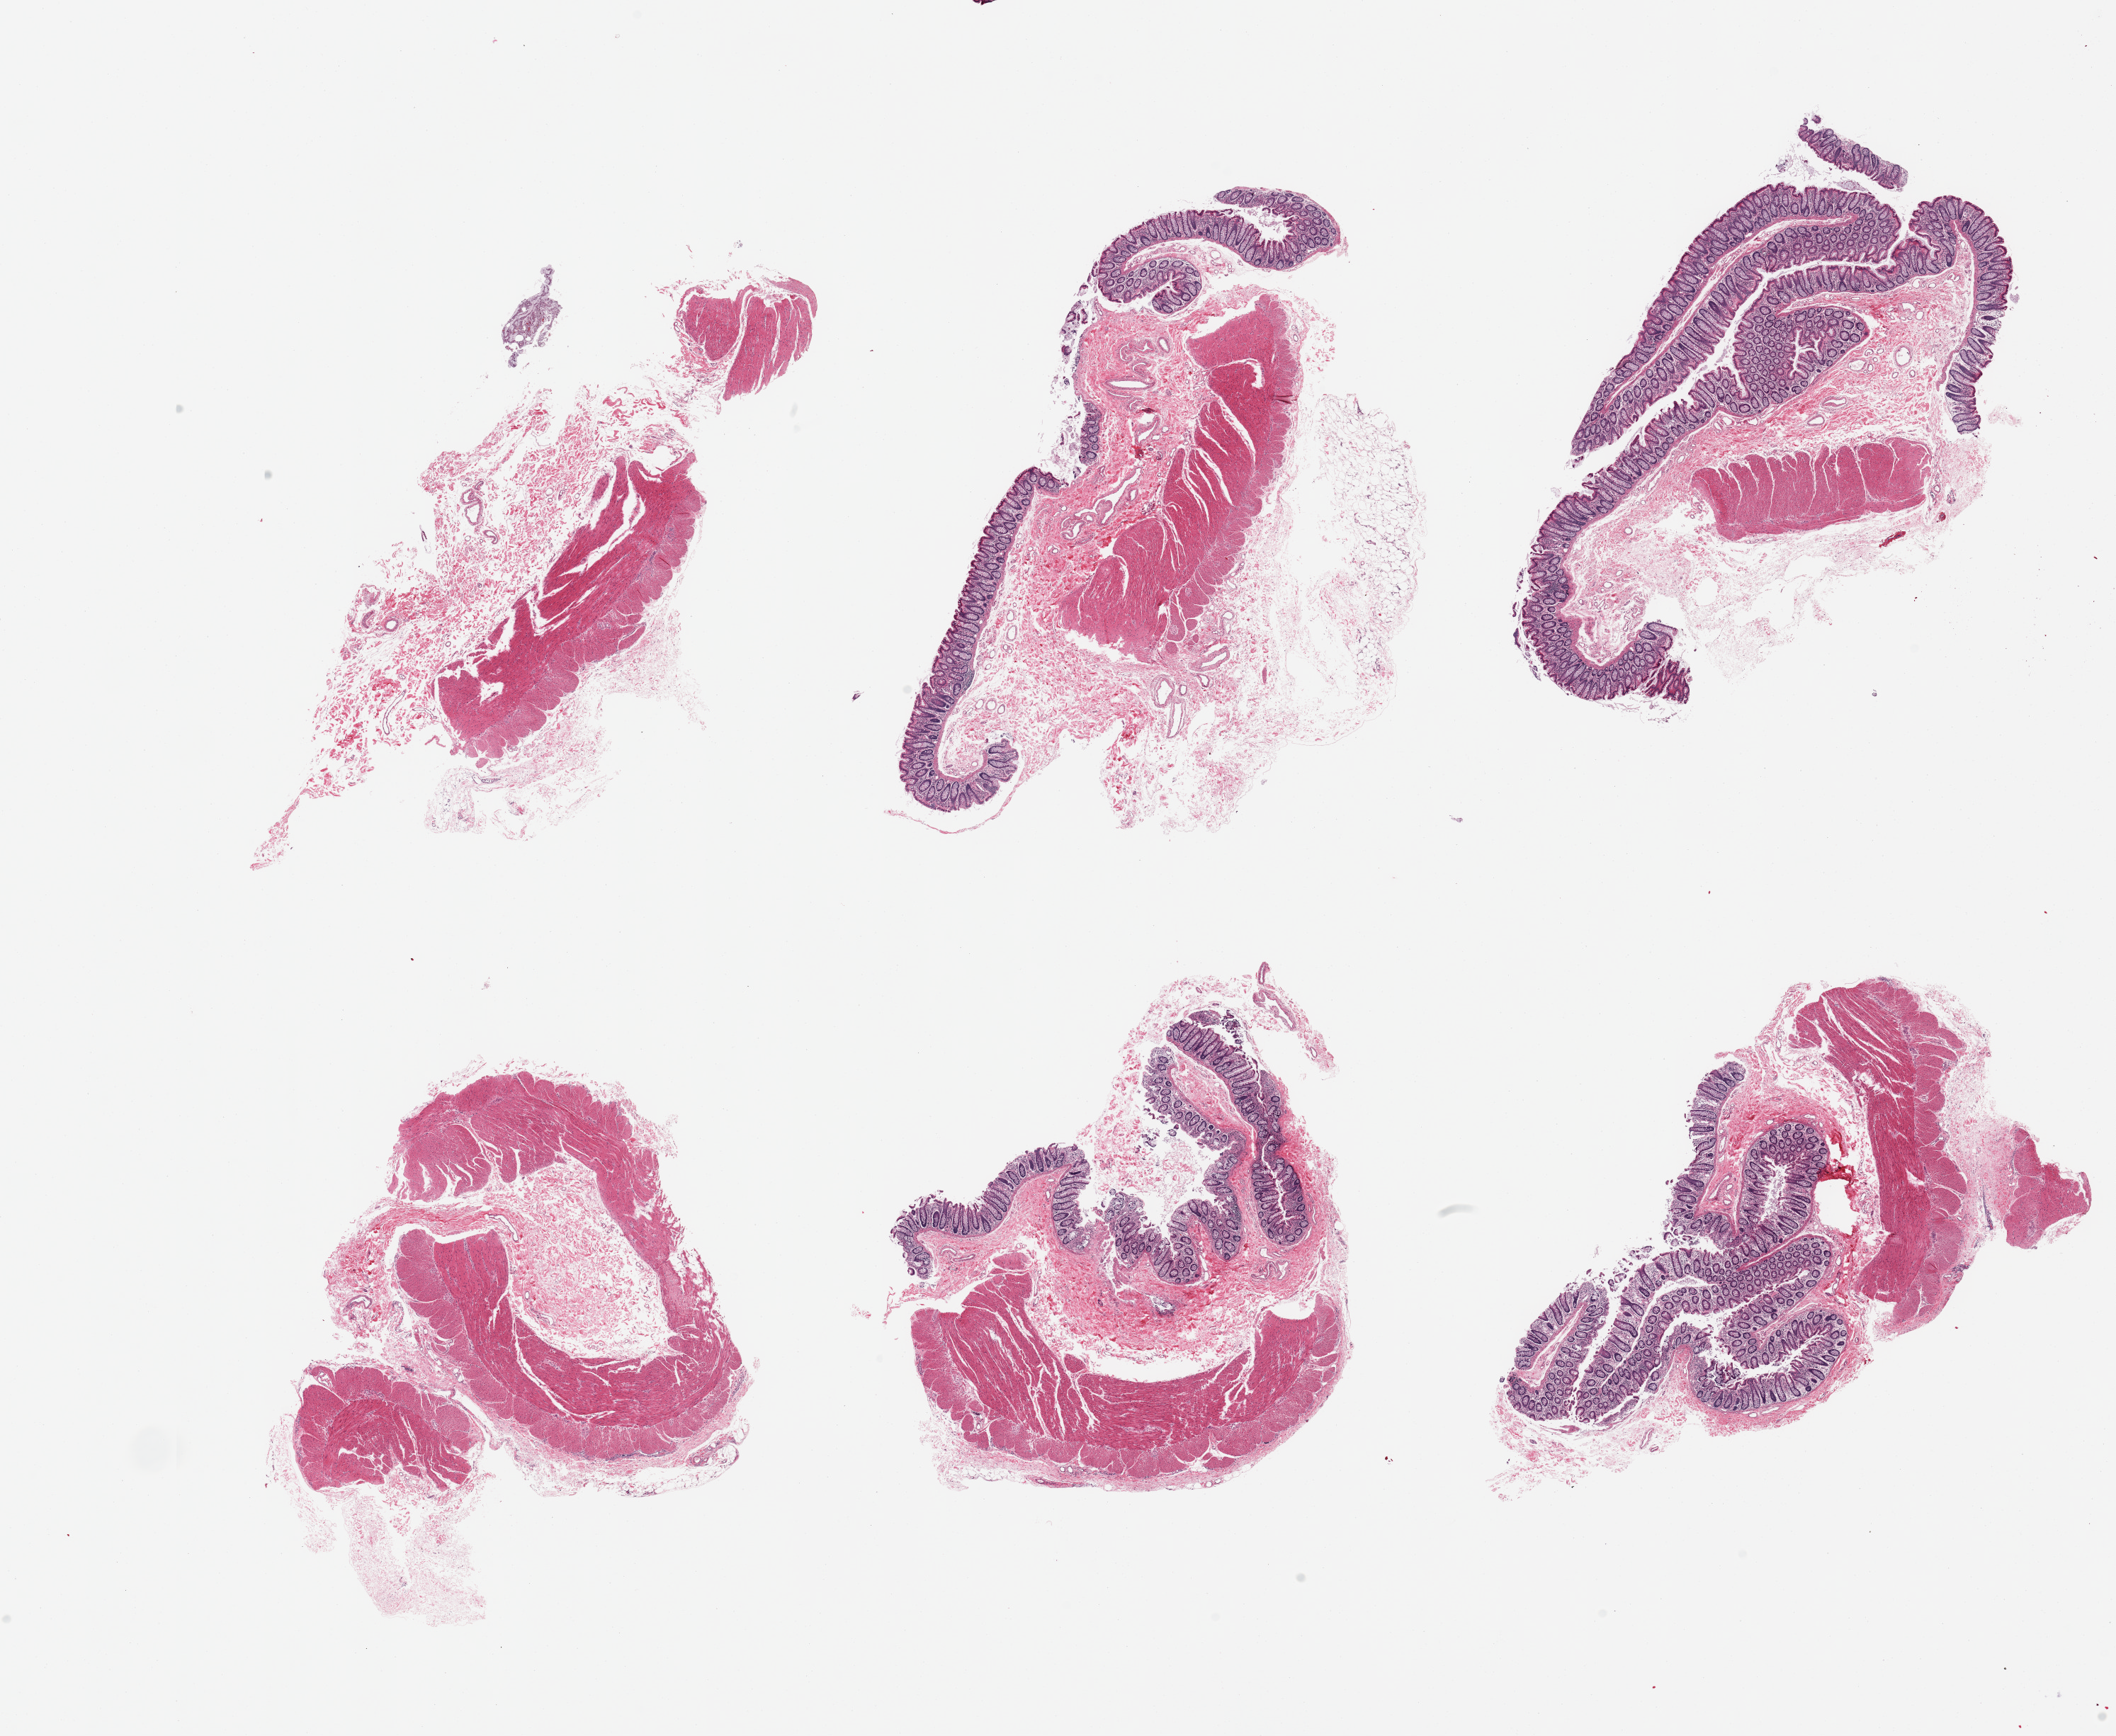
H&E whole-slide image — low-resolution overview of the scanned area, about 23.6 x 19.4 mm; PAXgene-fixed paraffin-embedded (PFPE) section; section of transverse colon (target tissue); tissue donor sample. Donor: female.
Review note (as recorded): 6 pieces: 2 without mucosa.